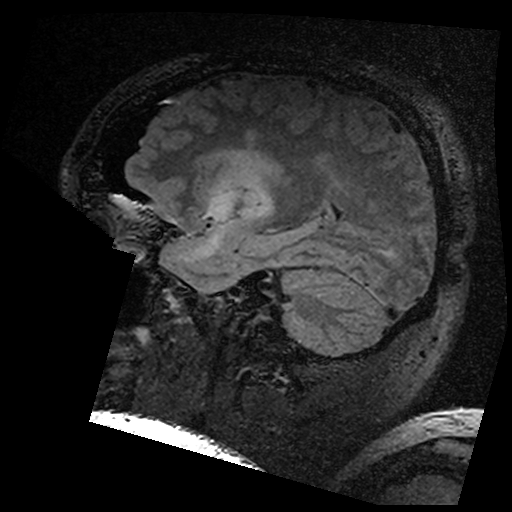
Brain MRI from a brain-tumour surgery series, one sagittal slice. Slice 117 of 176 in the series (ordered by position). T2 FLAIR. 512 × 512 image matrix, field of view 250 × 250 mm. Case-level facts recorded for this patient, not image findings: histopathology: Astrocytoma; WHO grade: 3; IDH mutation: yes; tumour location: Left Insular.
Annotated regions visible in this slice (expert manual segmentation):
- residual tumour: box from (x=198, y=146) to (x=287, y=200) px